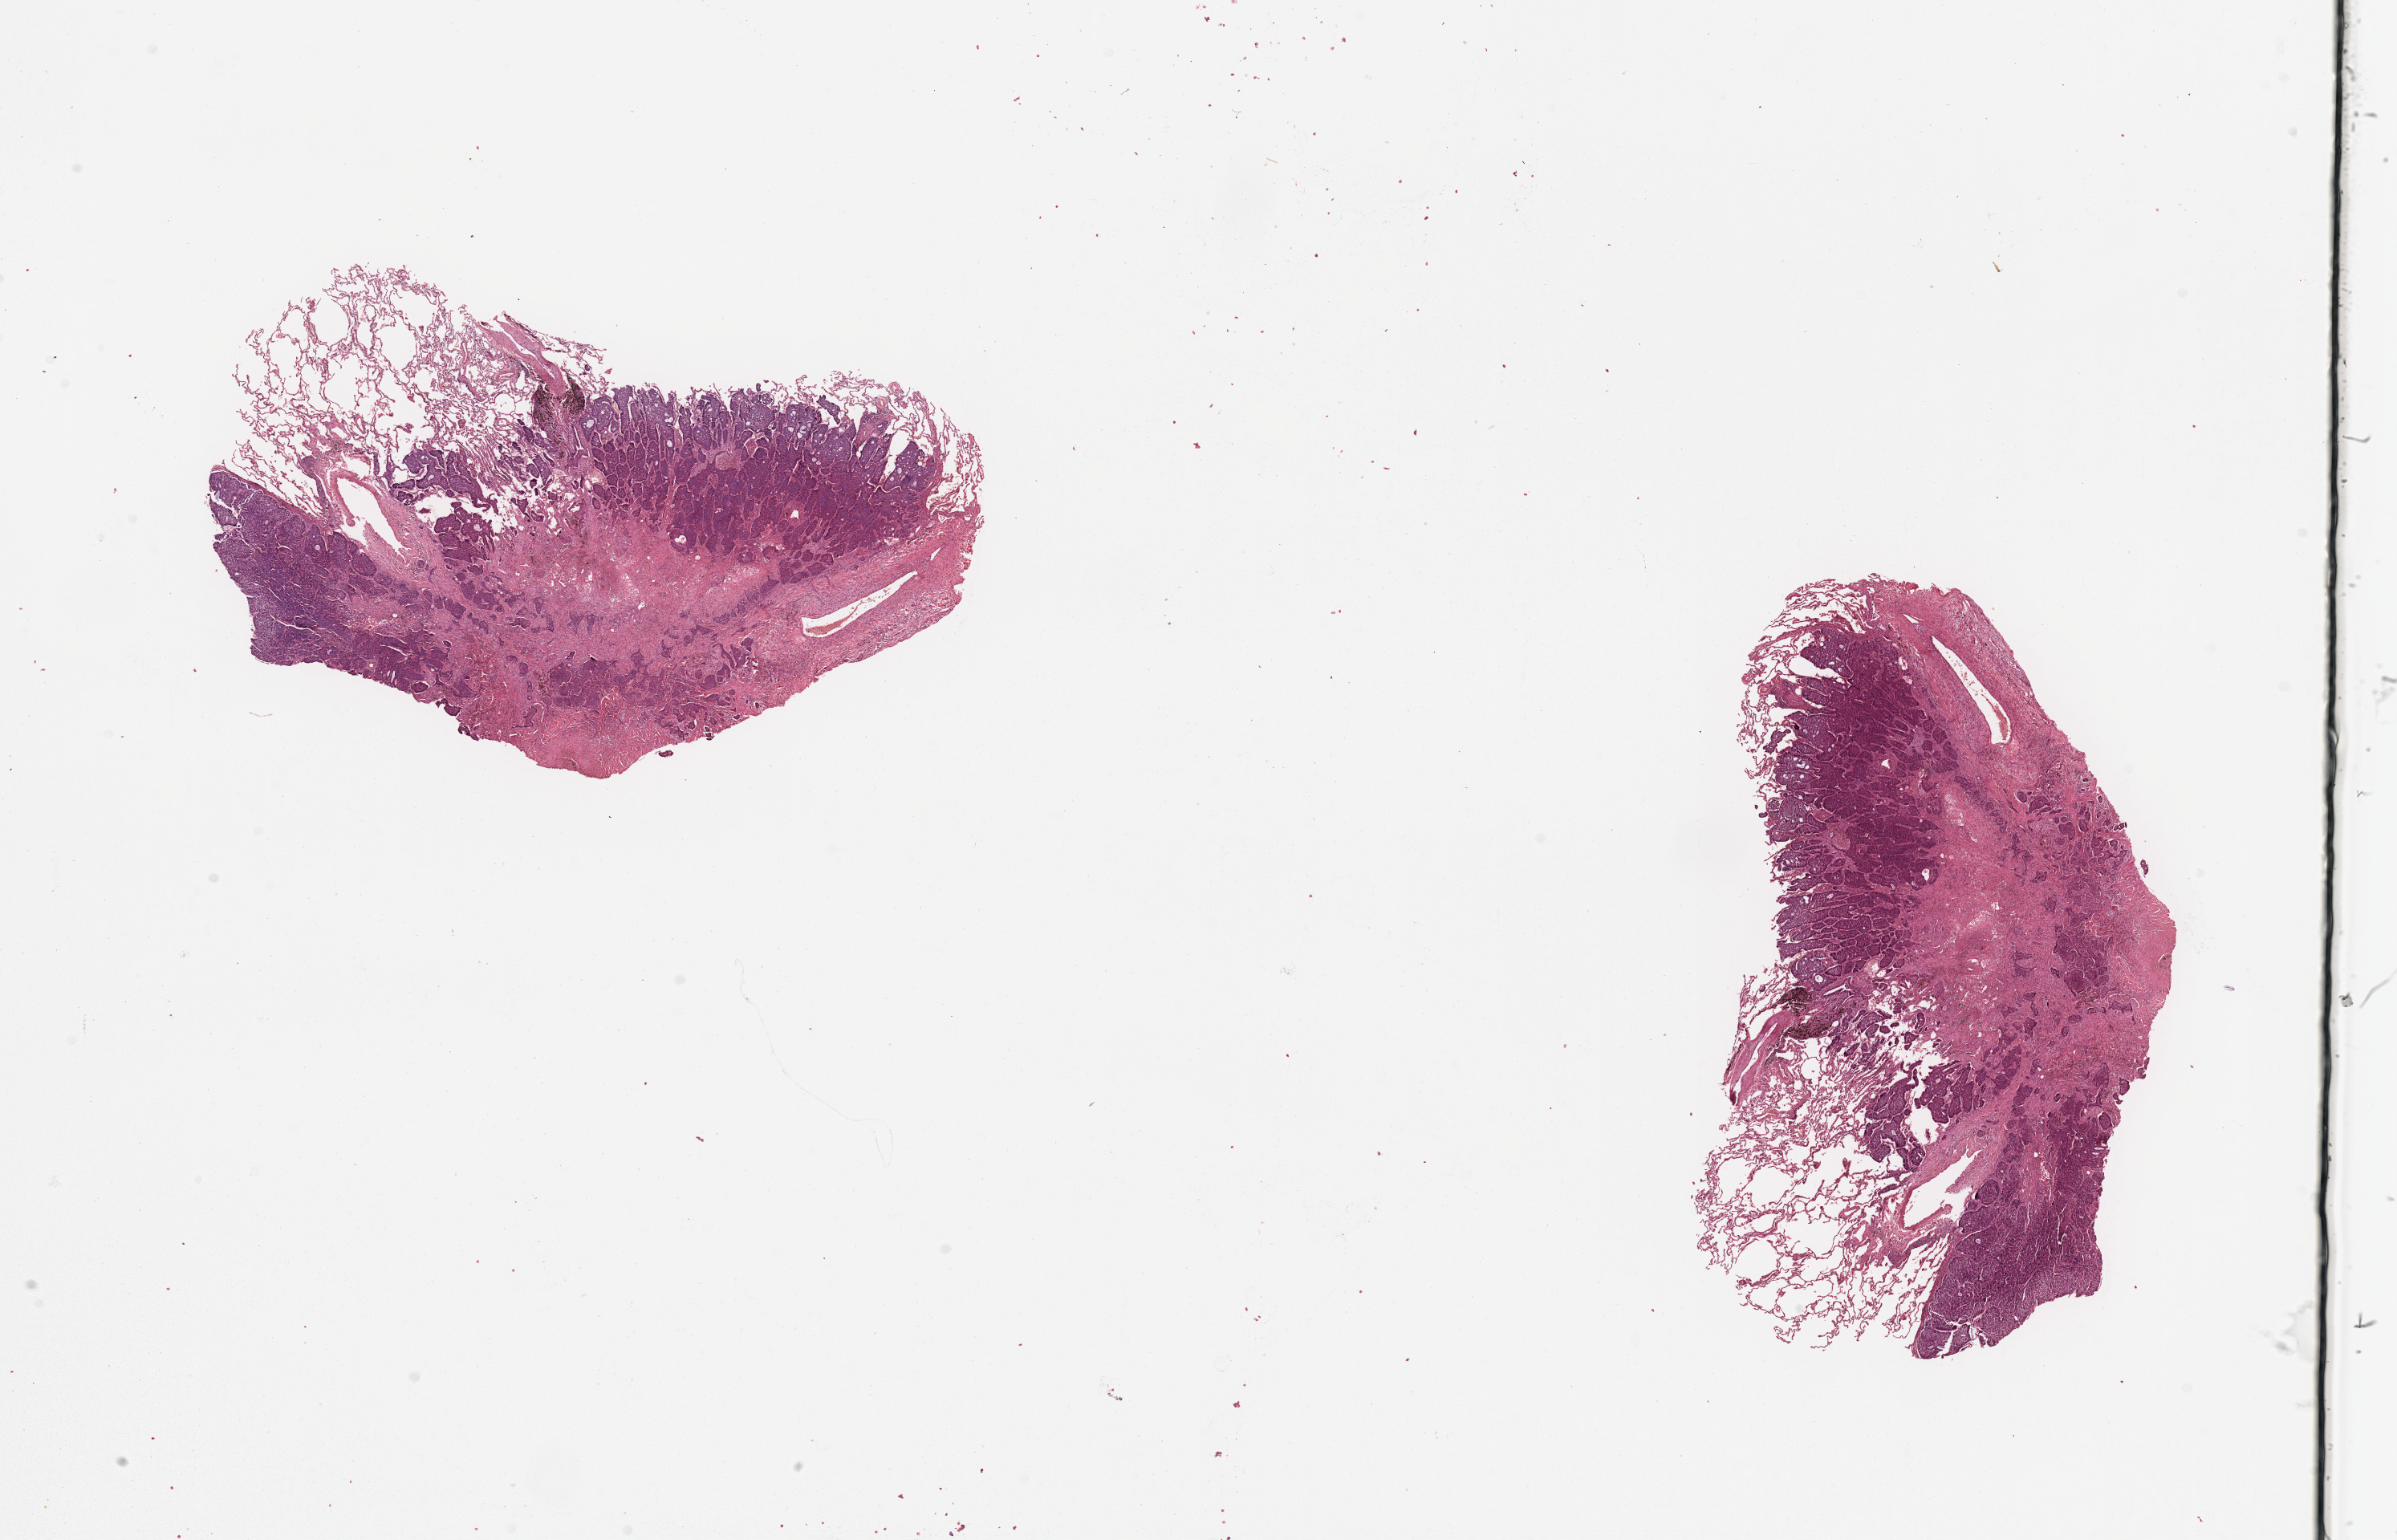
Whole-slide histology image, H&E-stained, whole scanned area (about 23.6 x 15.2 mm, from a 20x scan) shown as a low-resolution overview; tumour tissue sample, lung. Male, 66 y/o.
Patient diagnosis (cohort enrolment): squamous cell carcinoma (lung).